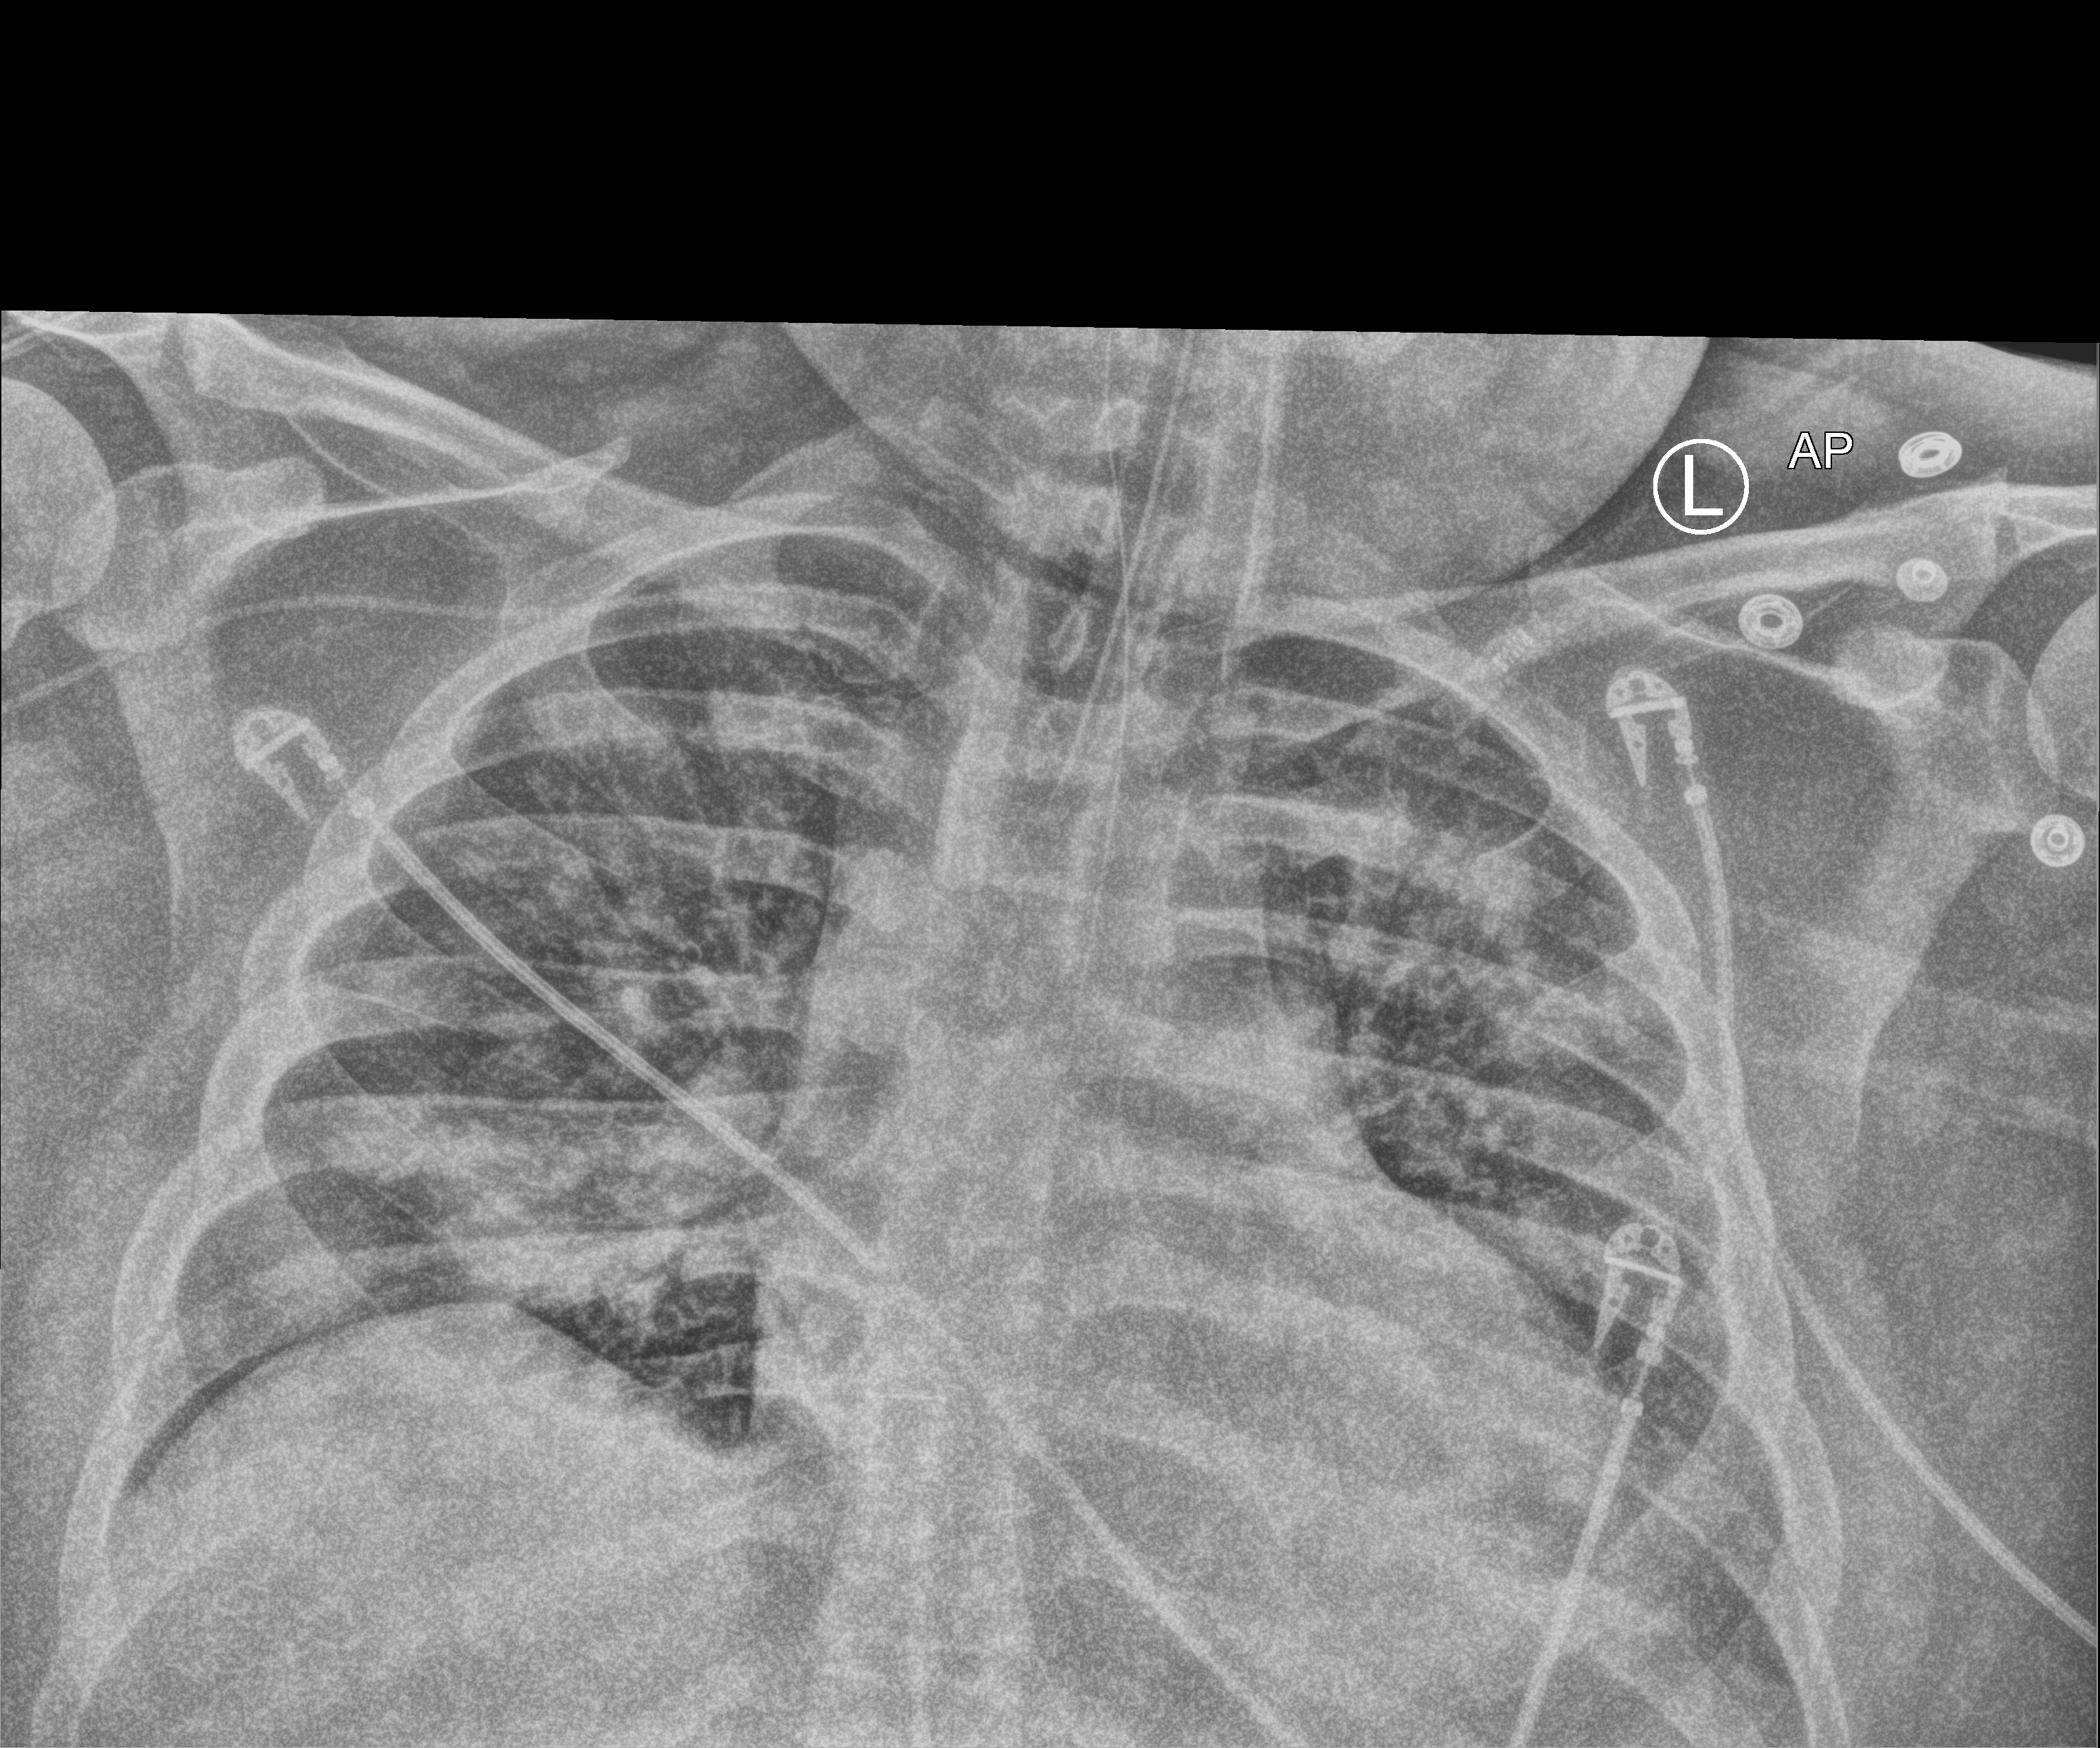
Bedside chest radiograph (computed radiography), anteroposterior (AP) projection. Patient hospitalised with COVID-19, aged 18–59 years.
Hospital-stay facts (about this admission, not read from this image; timing relative to this image not recorded):
- admitted to intensive care during this hospital stay: yes
- mechanically ventilated during this hospital stay: yes
- length of hospital stay: 10 days